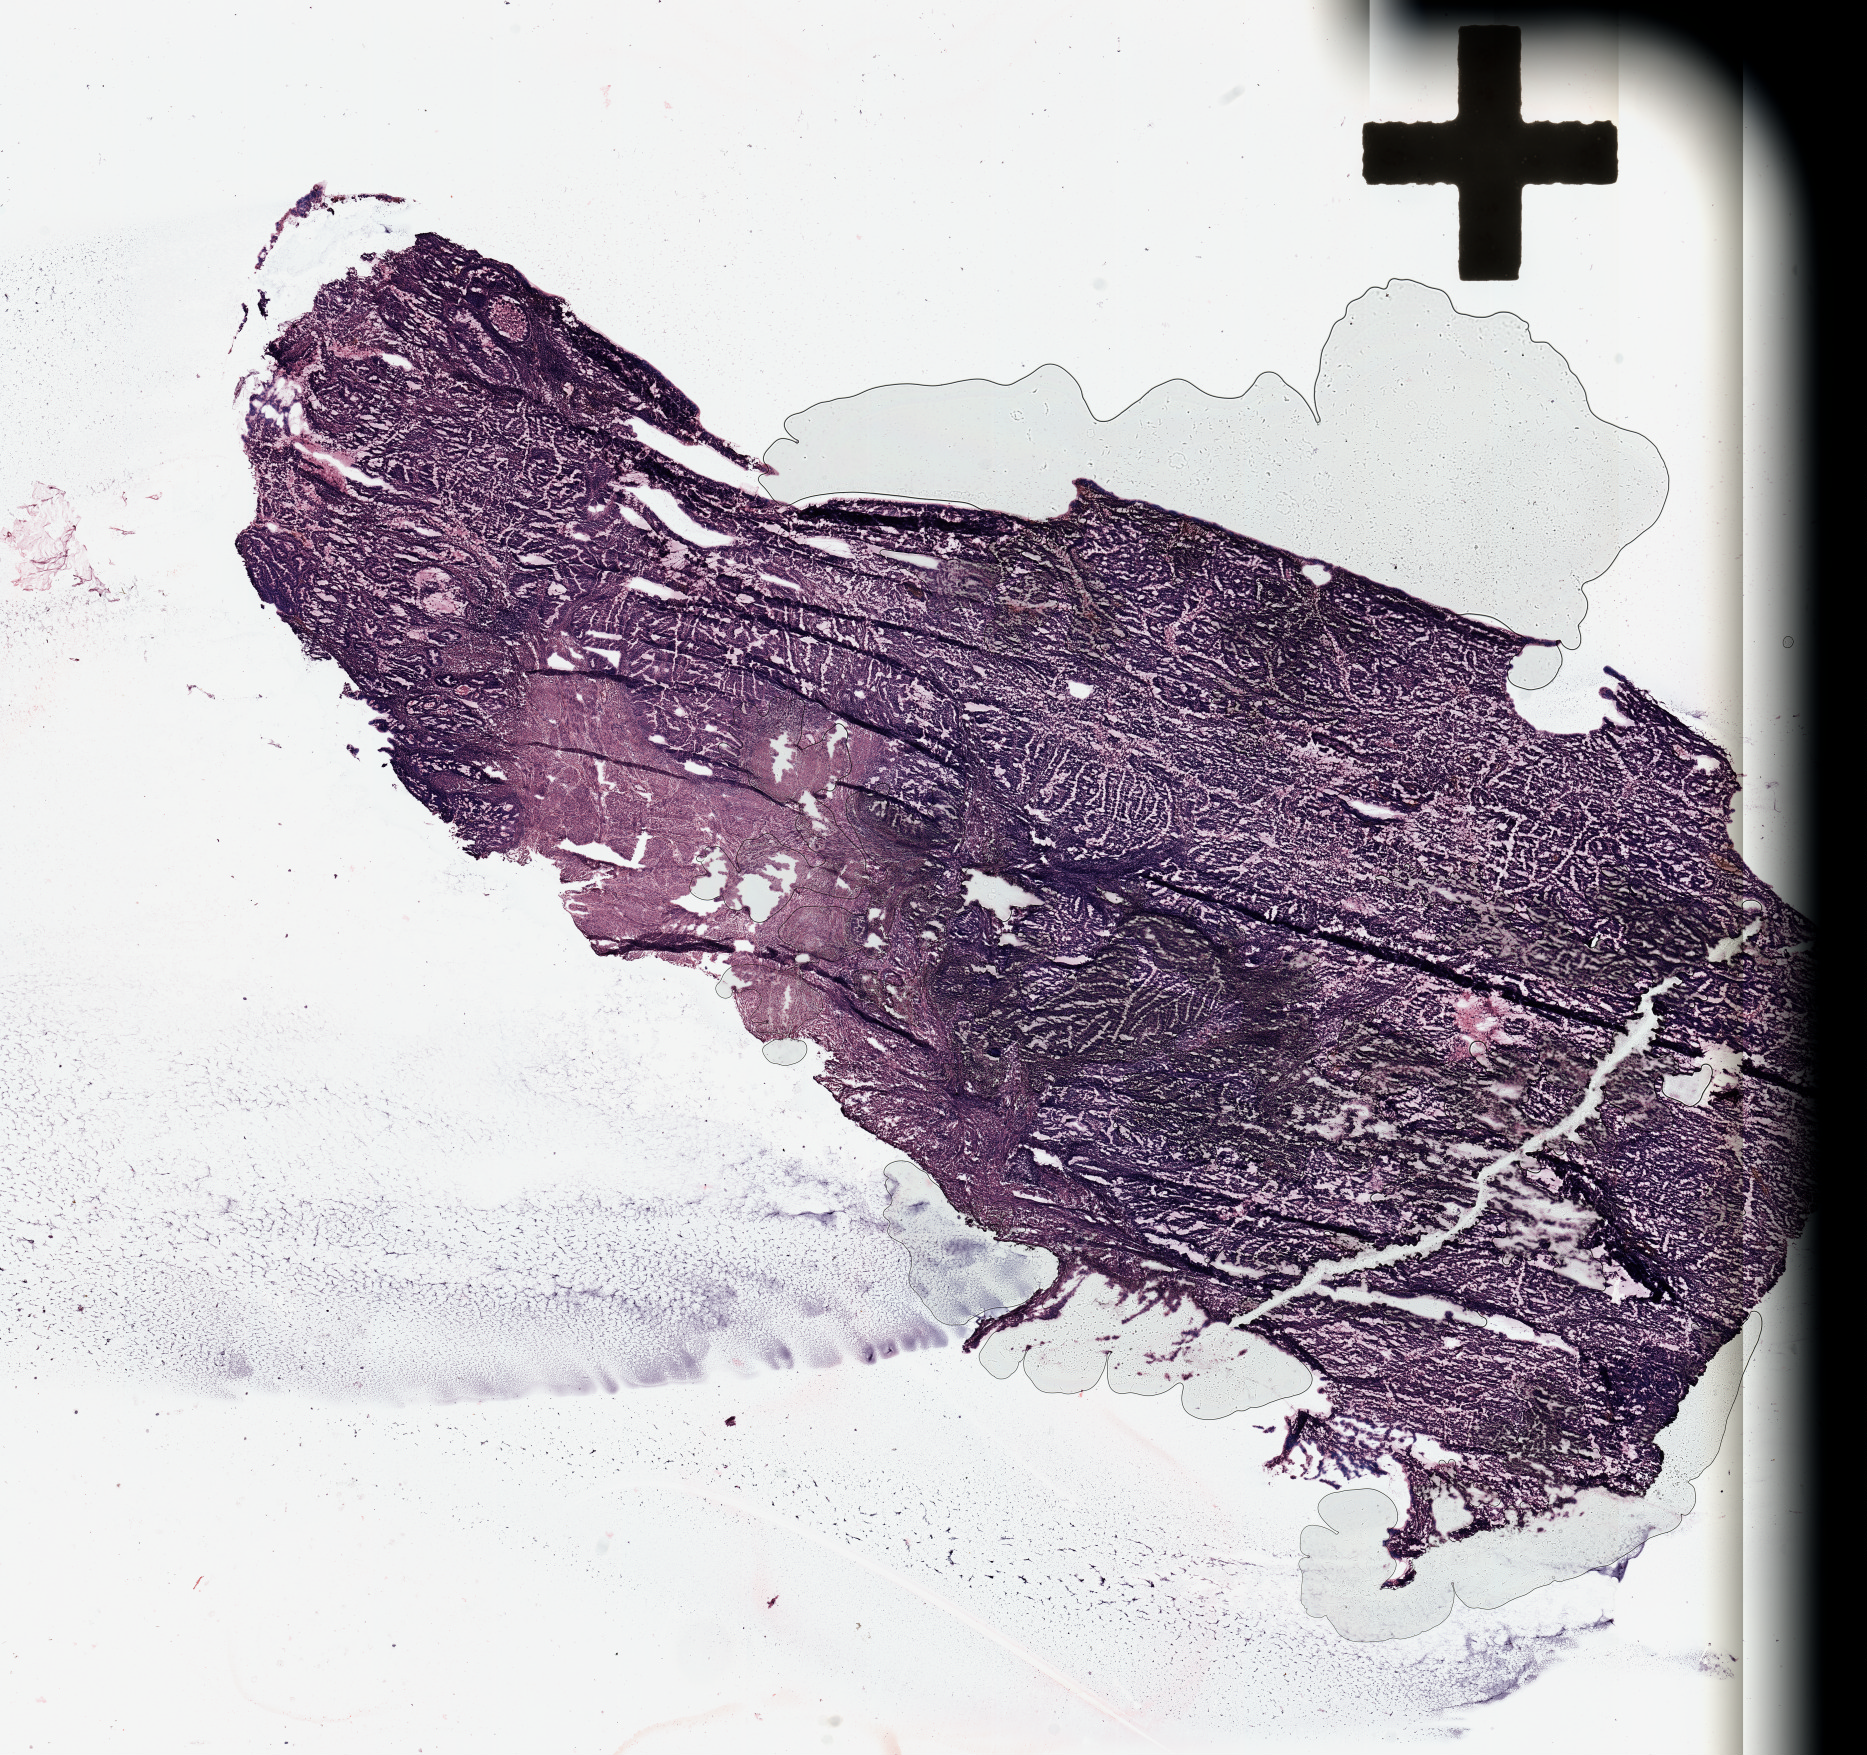
Whole-slide histology image, H&E-stained, low-resolution overview of the scanned area, about 14.8 x 13.9 mm, uterus, tumour tissue. 66-year-old female patient. Histologic grade: G2 (moderately differentiated).
AJCC pathologic stage: II. Diagnosis: Endometrioid adenocarcinoma, NOS.